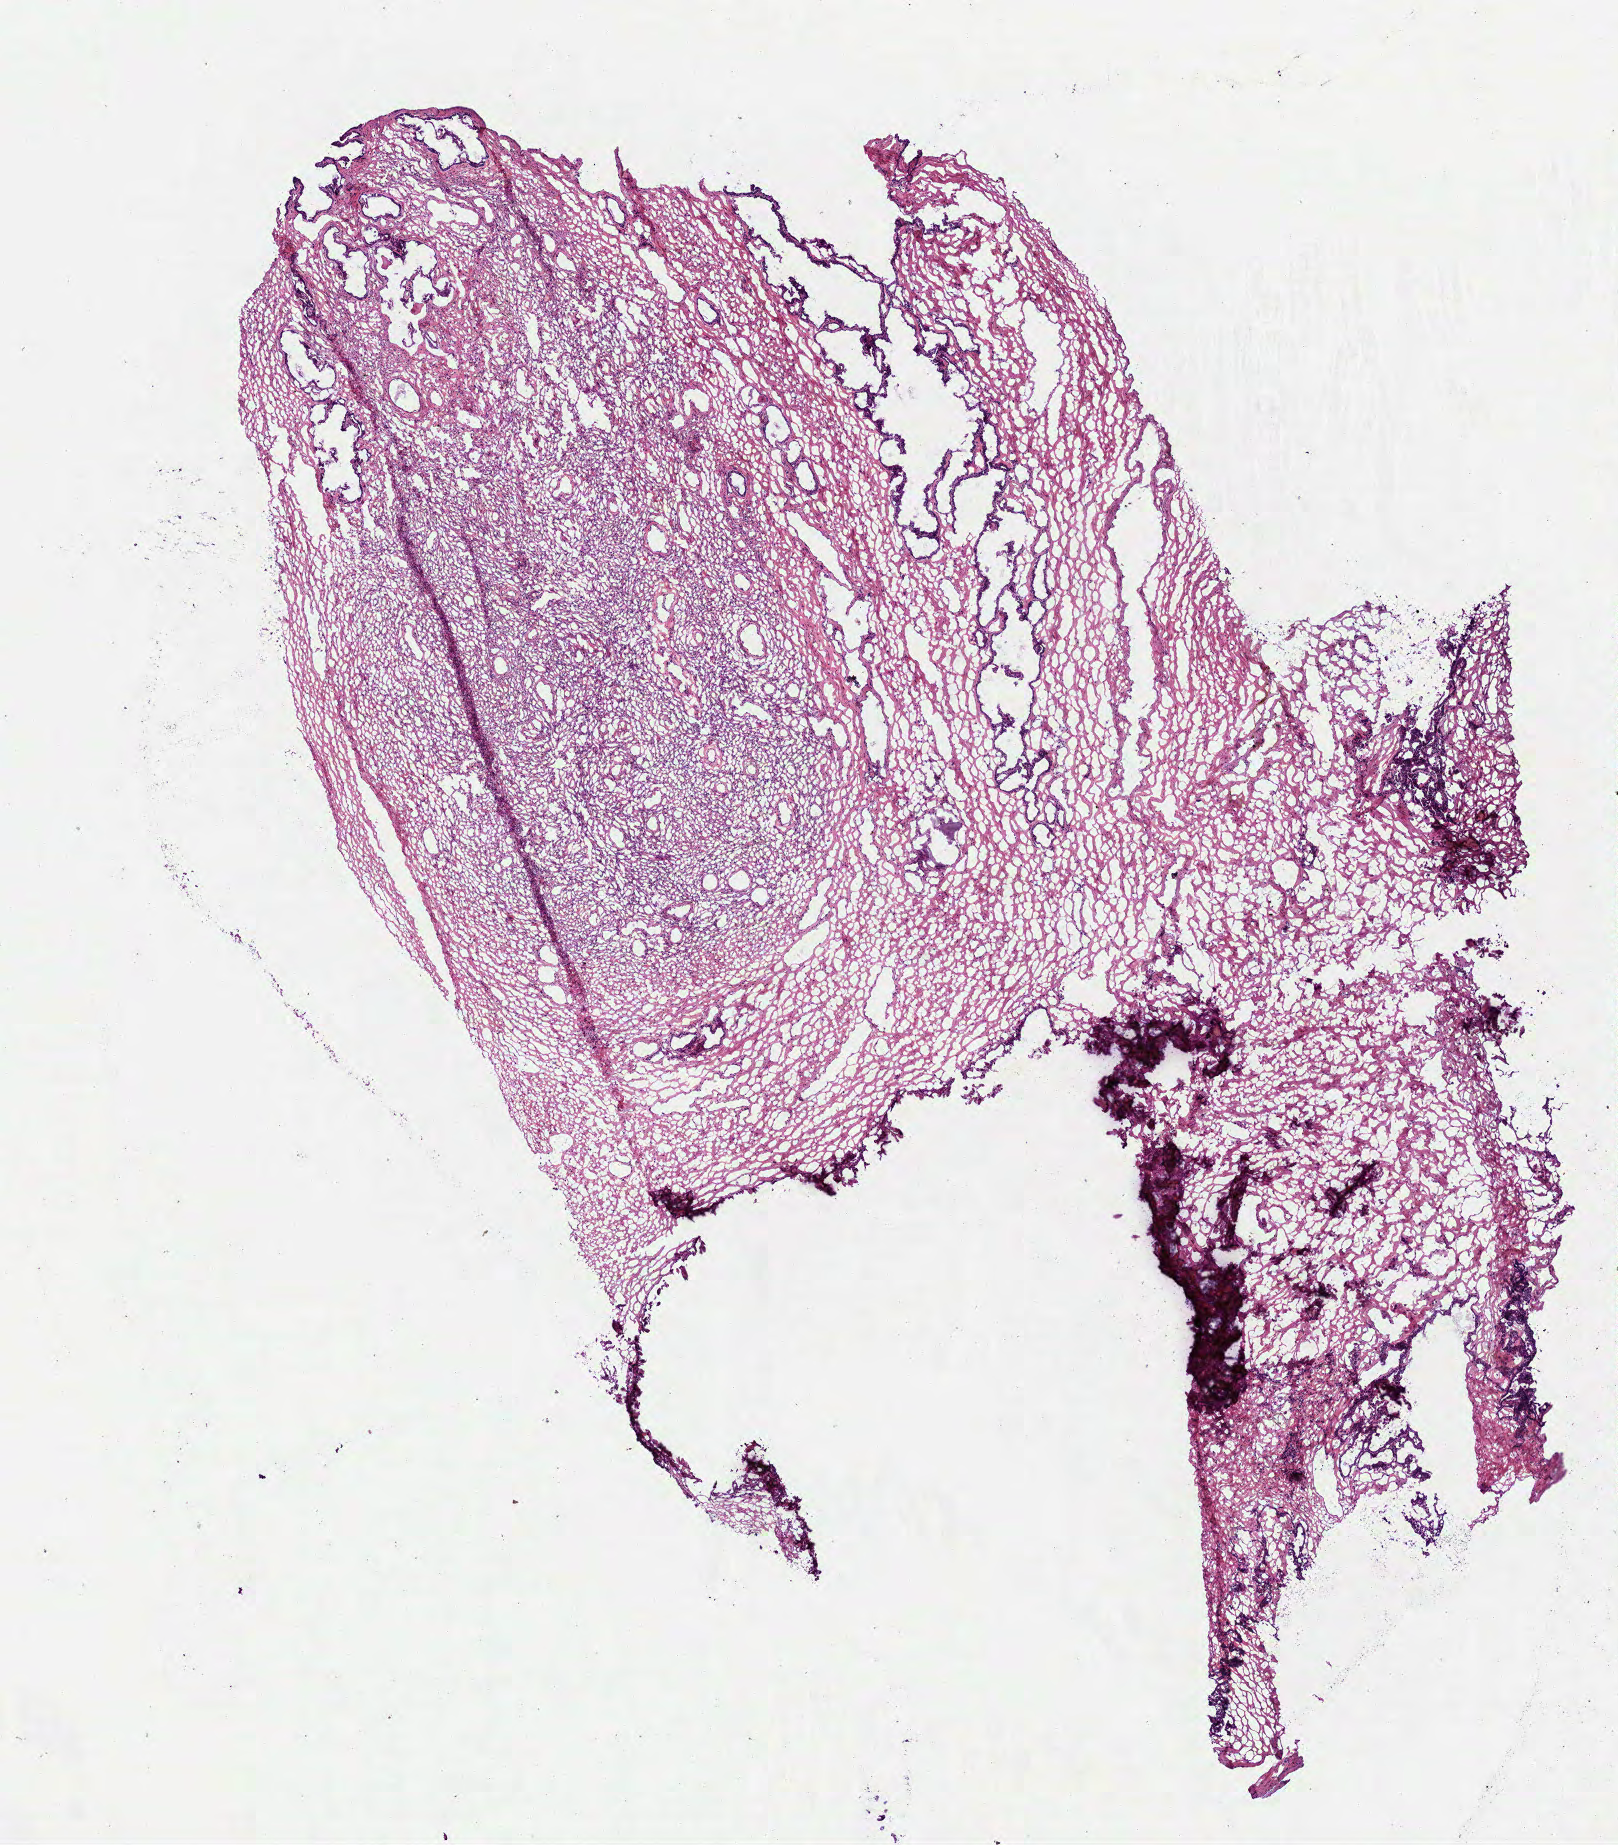
H&E whole-slide image, low-resolution overview of the scanned area, about 6.5 x 7.4 mm; frozen section; primary tumour sample from the prostate. Patient: male, age at initial diagnosis 67 years. Slide review estimates, as recorded: tumour cells 30%, tumour nuclei 0%.
Pathologic diagnosis: Acinar cell carcinoma.